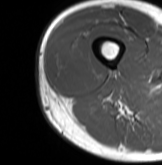
MRI of an extremity soft-tissue mass, one axial slice. Slice 20 of 61 in the series (ordered by position). MR volume resampled by the dataset authors to the PET/CT grid (not the native acquisition matrix). 3.27 mm slice thickness. 162 × 165 image matrix, field of view 158 × 161 mm. Male patient. Case-level facts recorded for this patient, not image findings: histological type: poorly differentiated synovial sarcoma; grade: high; site of the primary tumour: right buttock.
Structures marked on this image (expert contour drawn on MRI and transferred to this co-registered scan by the dataset authors):
- gross tumour volume including surrounding oedema: bounding box (x1, y1, x2, y2) in pixels: (52, 43, 99, 92)